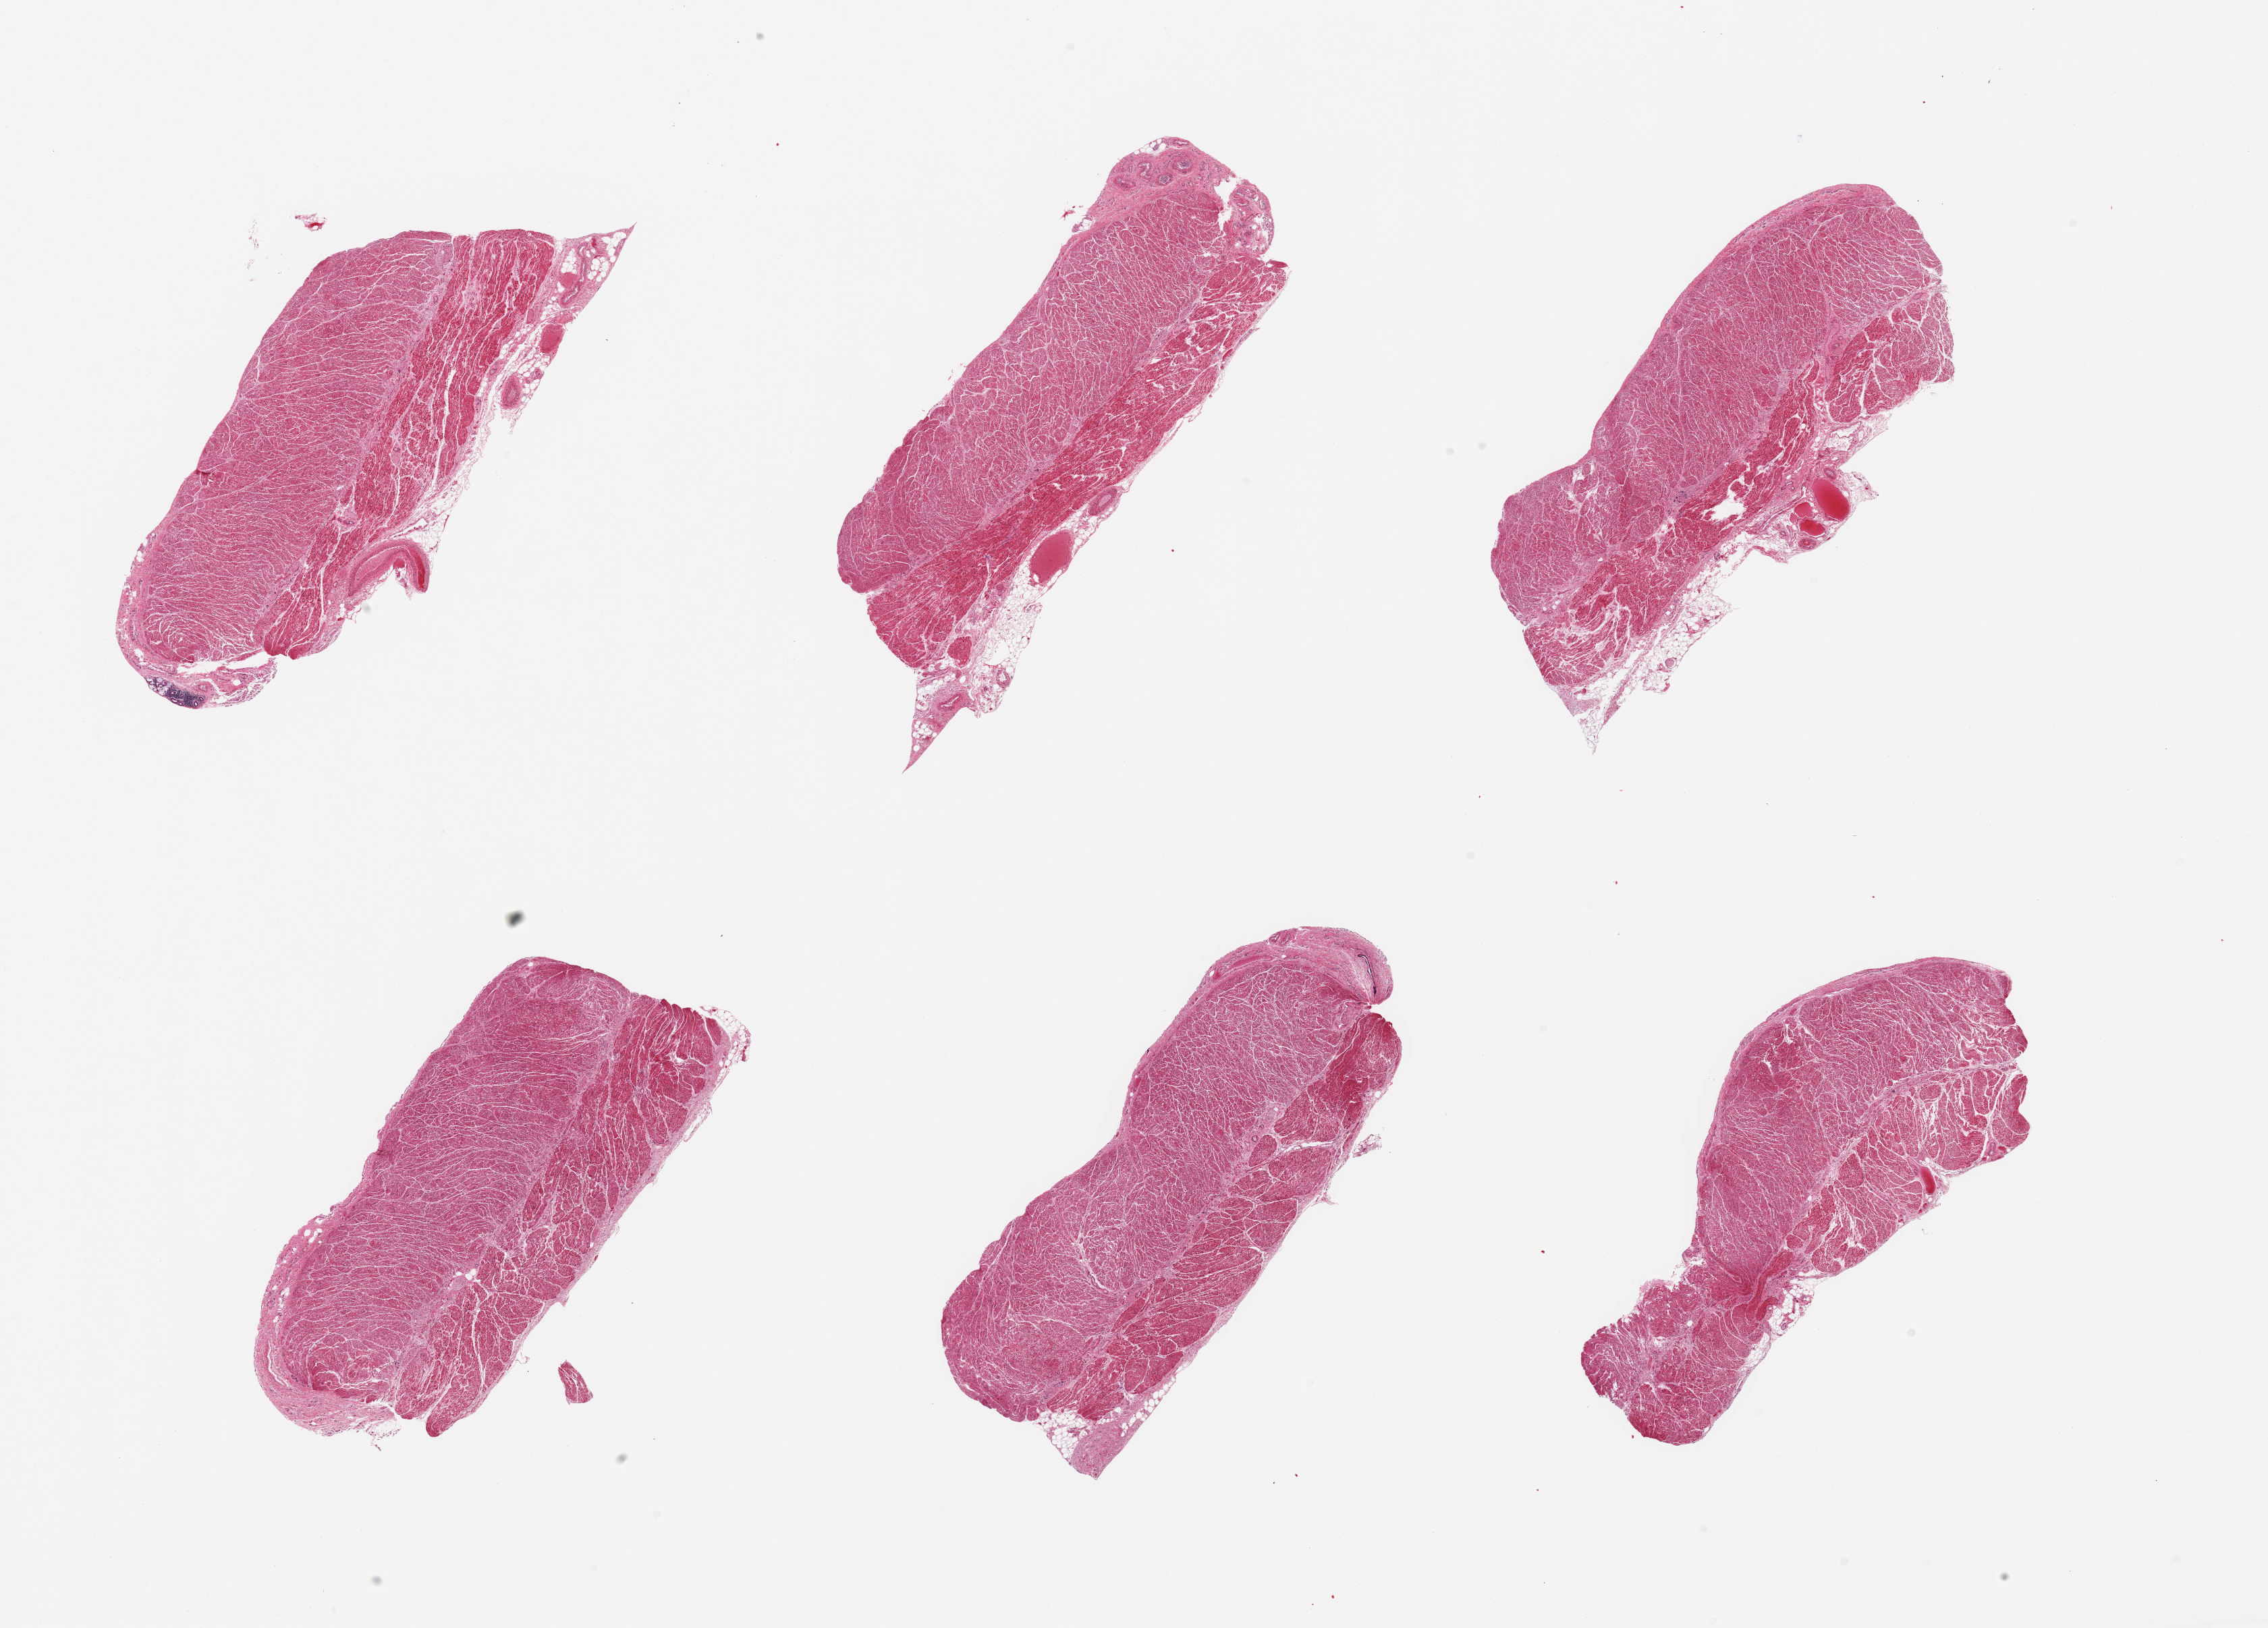
Hematoxylin and eosin (H&E) whole-slide image, brightfield, shown as a low-resolution overview of the whole scanned area (about 26.6 x 19.1 mm); PAXgene-fixed, paraffin-embedded tissue; section of gastroesophageal junction (target tissue); tissue donor sample. Donor sex: female.
Review note (as recorded): 6 pieces; well dissected target muscle.